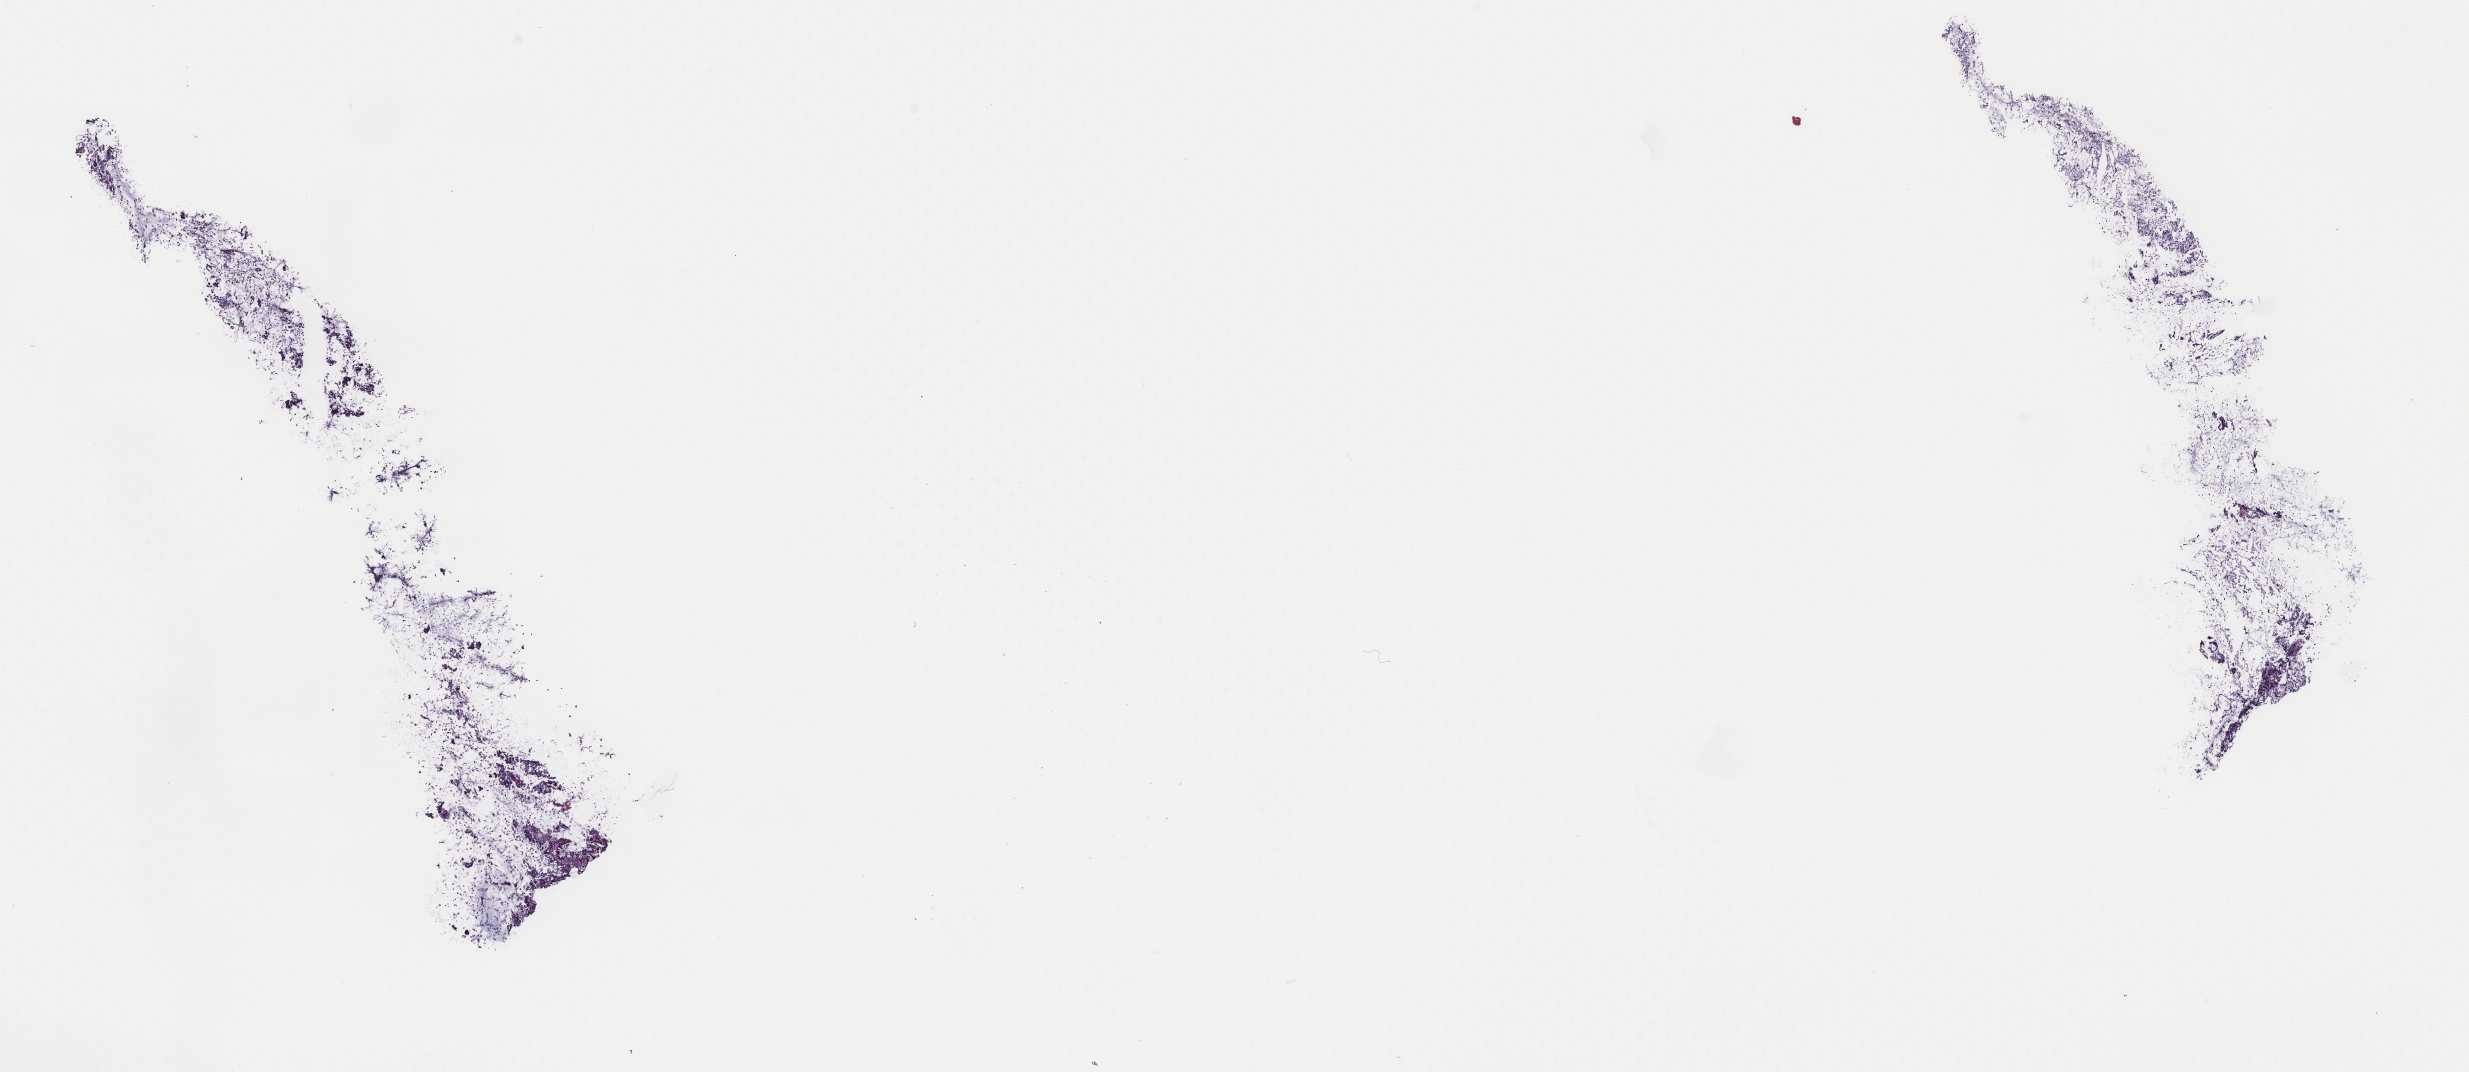
Whole-slide histology image, H&E-stained — low-resolution overview of the scanned area, about 19.6 x 8.5 mm (from a 40x scan), frozen section, sample: primary tumour, lung. Patient: male, age at initial diagnosis 74 years. Slide review estimates, as recorded: tumour cells 100%, tumour nuclei 80%, normal cells 0%, stromal cells 0%, necrosis 0%. Inflammatory infiltration, as recorded: lymphocyte infiltration 2%, monocyte infiltration 4%, neutrophil infiltration 0%.
Pathologic diagnosis: Adenocarcinoma, NOS (upper lobe, lung). AJCC pathologic stage: IIB (7th edition).